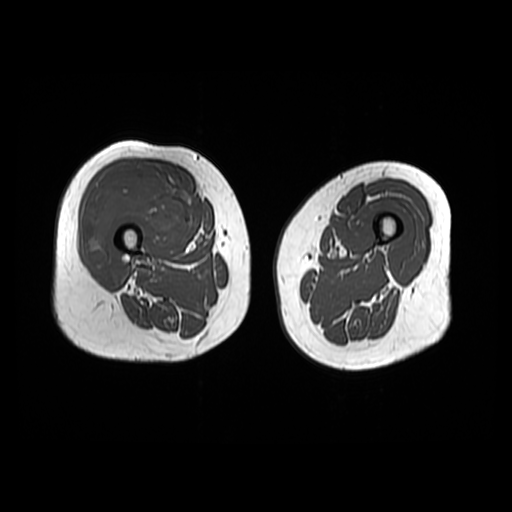
MRI of an extremity soft-tissue mass, one axial slice; slice 22 of 48 in the series (ordered by position); 6 mm slice thickness; 512 × 512 image matrix, field of view 440 × 440 mm. Female patient. From the clinical record (not read from this slice): histological type: pleiomorphic undifferentiated sarcoma; grade: high; site of the primary tumour: right quadricep.
Outlined on this slice (manually delineated by an expert):
- gross tumour volume including surrounding oedema: box from (x=84, y=164) to (x=183, y=267) px
- gross tumour volume (mass): (x=84, y=164)–(x=183, y=267)